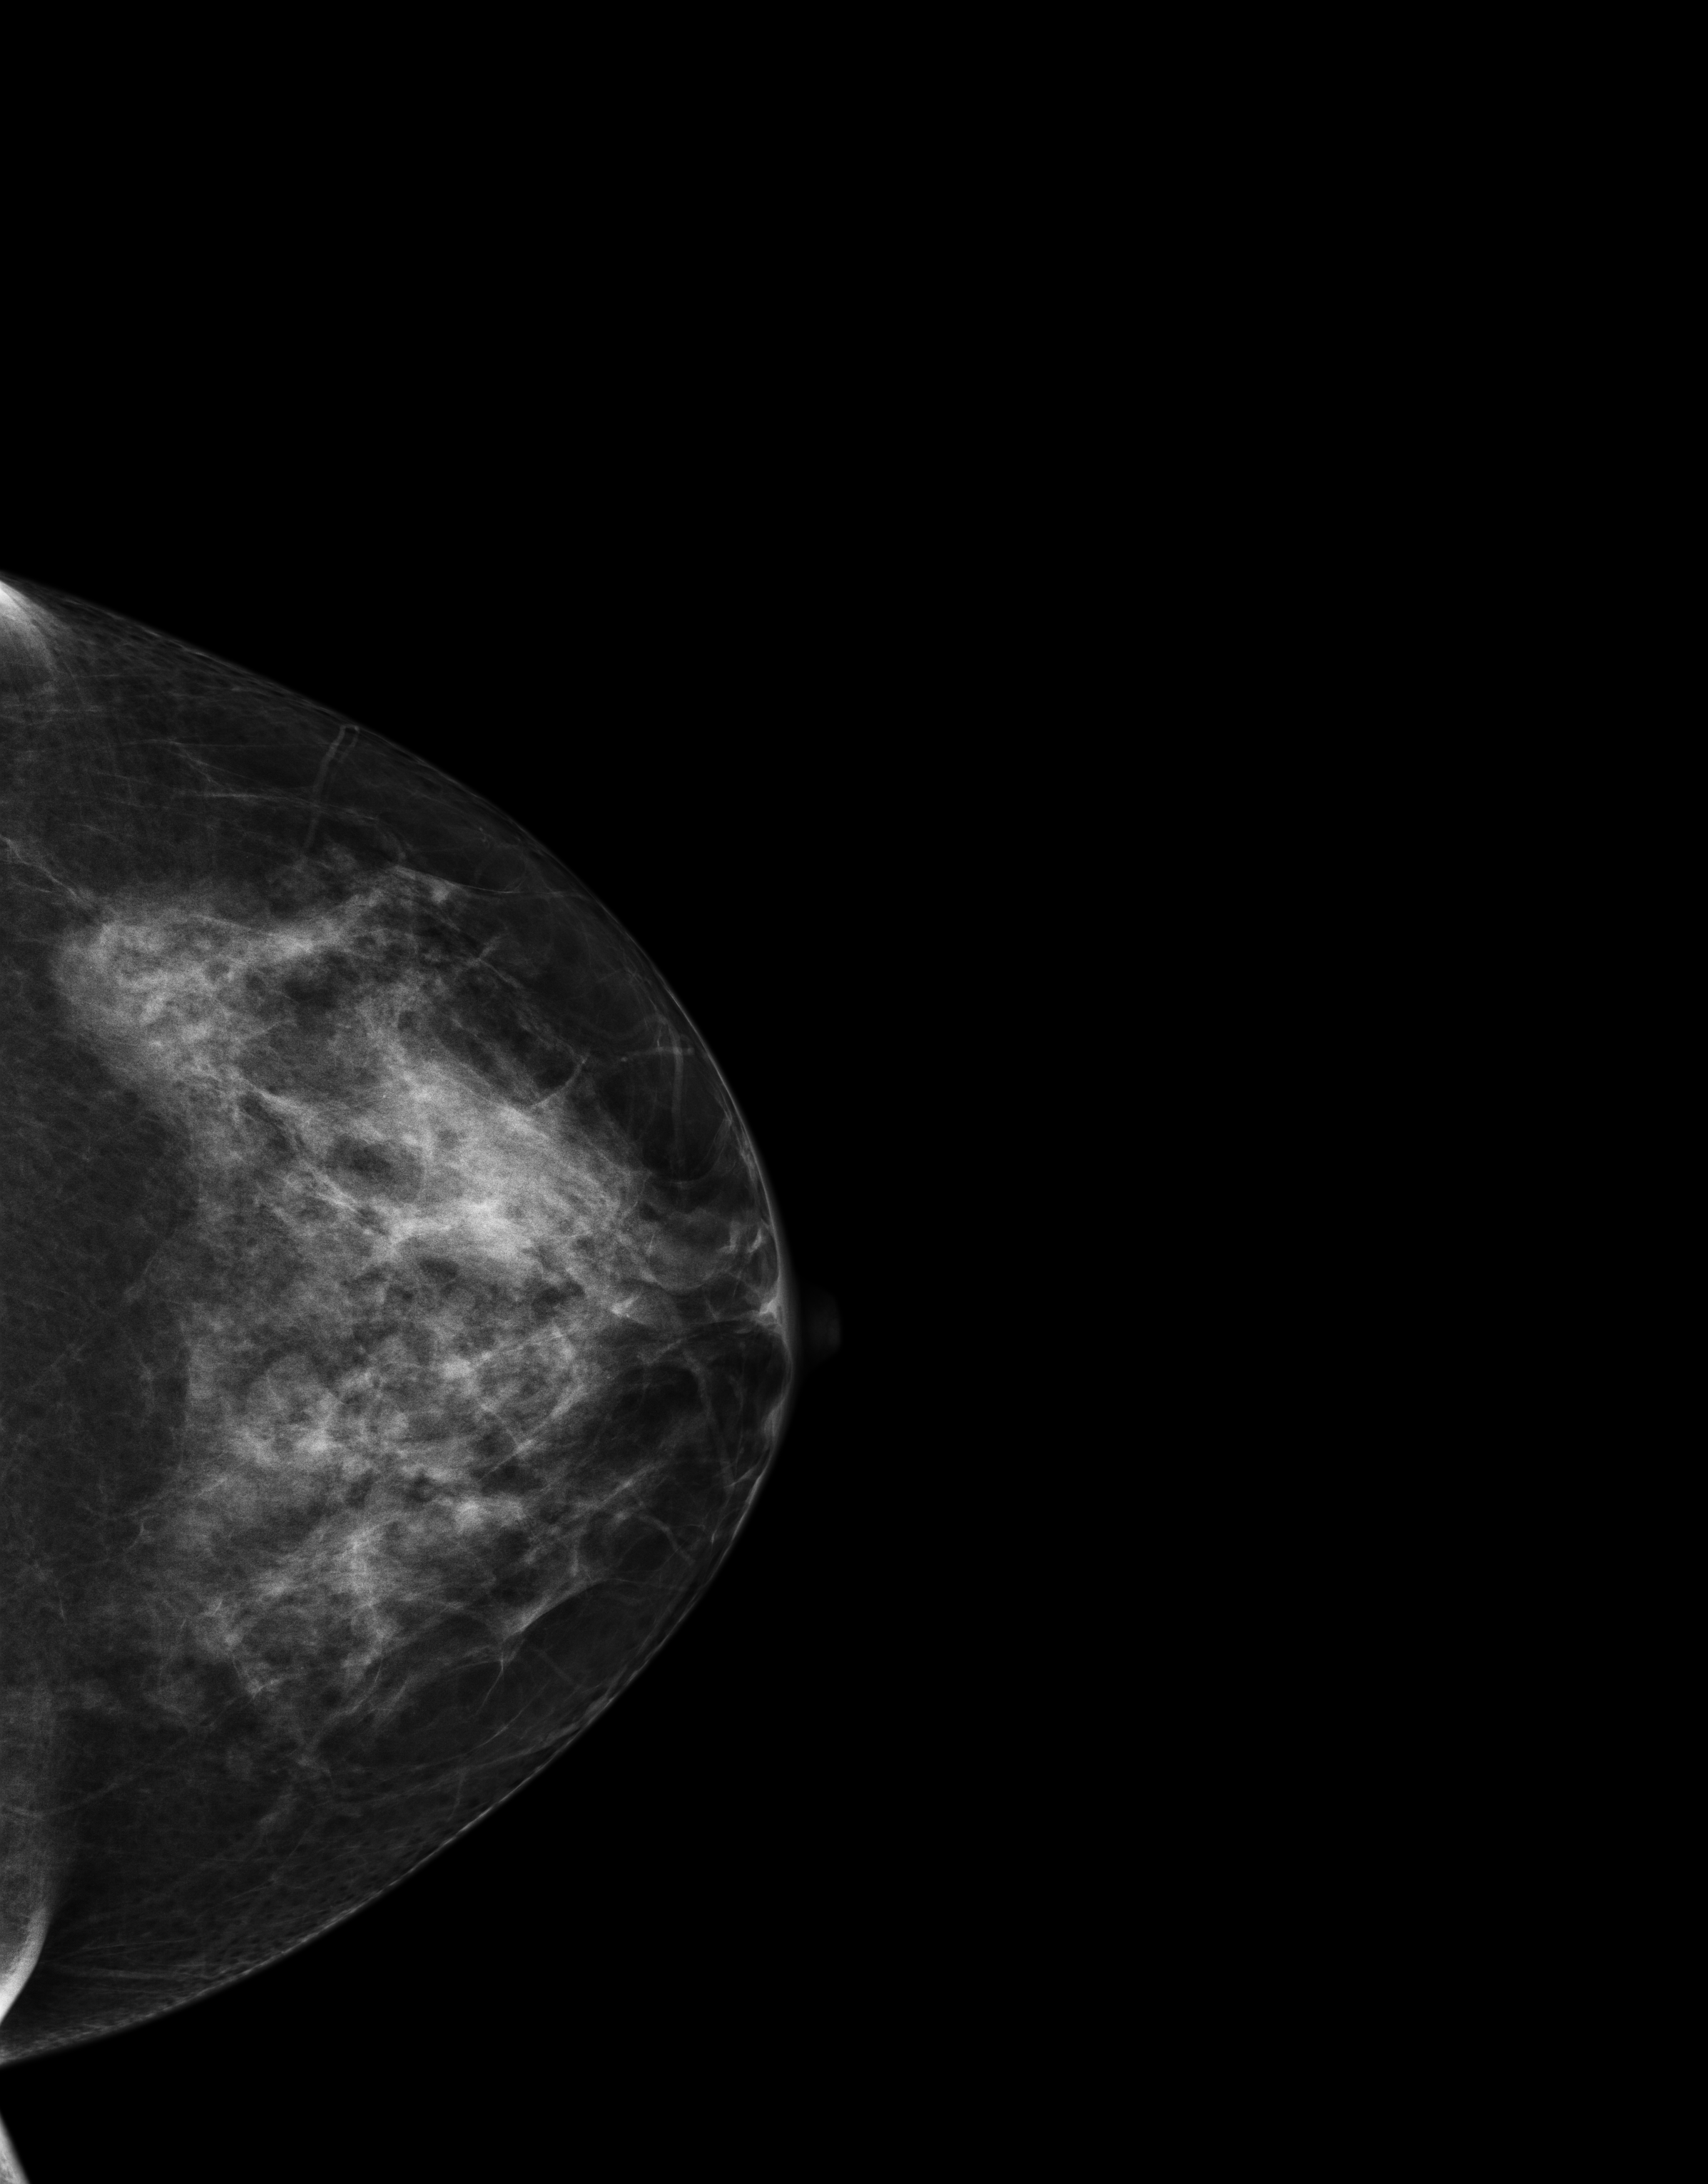
Annual screening mammography examination, compressed breast thickness 70 mm. Patient aged 46 years (female).
Image type: full-field digital mammogram. Breast: left. Projection: craniocaudal (CC) view.